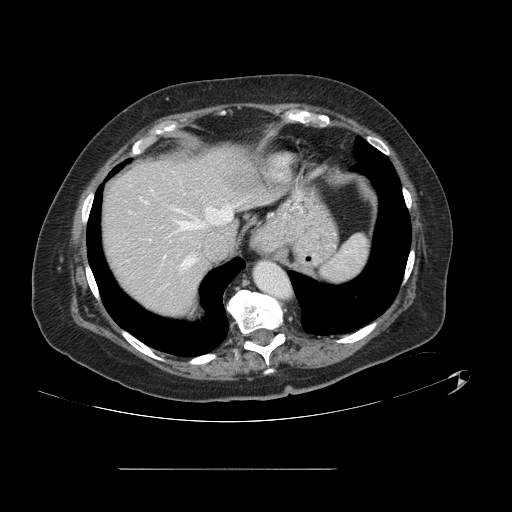
Contrast-enhanced abdominal CT, one axial slice; position 112 of 148 along the scan axis; 120 kVp; soft-tissue window (W 400 / L 40 HU); 512 × 512 image matrix, field of view 439 × 439 mm. Female patient, age 75 years. From the clinical record (not read from this slice): diagnosis: colorectal cancer liver metastases, imaged before liver resection; multiple liver metastases: no; largest metastasis: 2.4 cm; disease in both lobes: no.
Annotated regions visible in this slice (expert manual segmentation):
- hepatic veins: bounding box (x1, y1, x2, y2) in pixels: (172, 204, 239, 270)
- liver: (102, 144, 264, 317)
- planned liver remnant (the part of the liver to remain after resection): (102, 144, 263, 317)